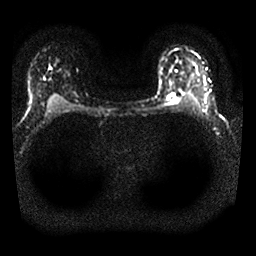
Breast MRI, one axial slice; position 20 of 25 along the scan axis; diffusion-weighted series; image 2 of 4 stored at this slice position (different b-values; order by instance number); 1.5 T; 256 × 256 image matrix, field of view 310 × 310 mm. Female patient.
Outlined on this slice (manually delineated by an expert):
- tumour on diffusion-weighted imaging: bounding box <167,93,178,103> (left, top, right, bottom; pixels)